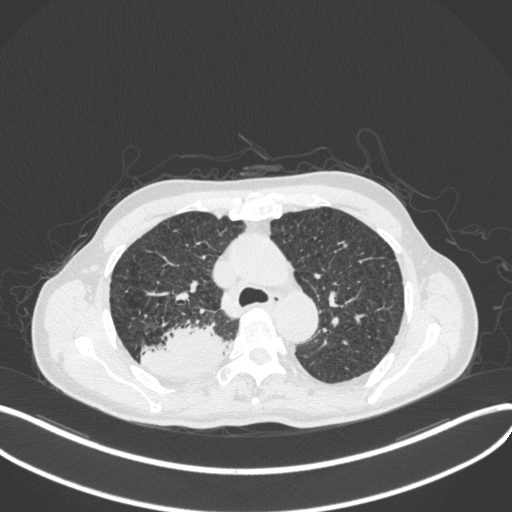
Chest CT, one axial slice. Position 318 of 423 along the scan axis. Reconstruction kernel B31f. Lung window (W 1500 / L -600 HU). 1 mm slice thickness. 512 × 512 image matrix, field of view 400 × 400 mm. Male patient, age 79 years. Case-level facts recorded for this patient, not image findings: clinical TNM (as recorded): T3 N0 M0.
Outlined on this slice (rectangle marked by the reading radiologist):
- lung tumour (recorded histology: adenocarcinoma): box from (x=139, y=322) to (x=231, y=378) px